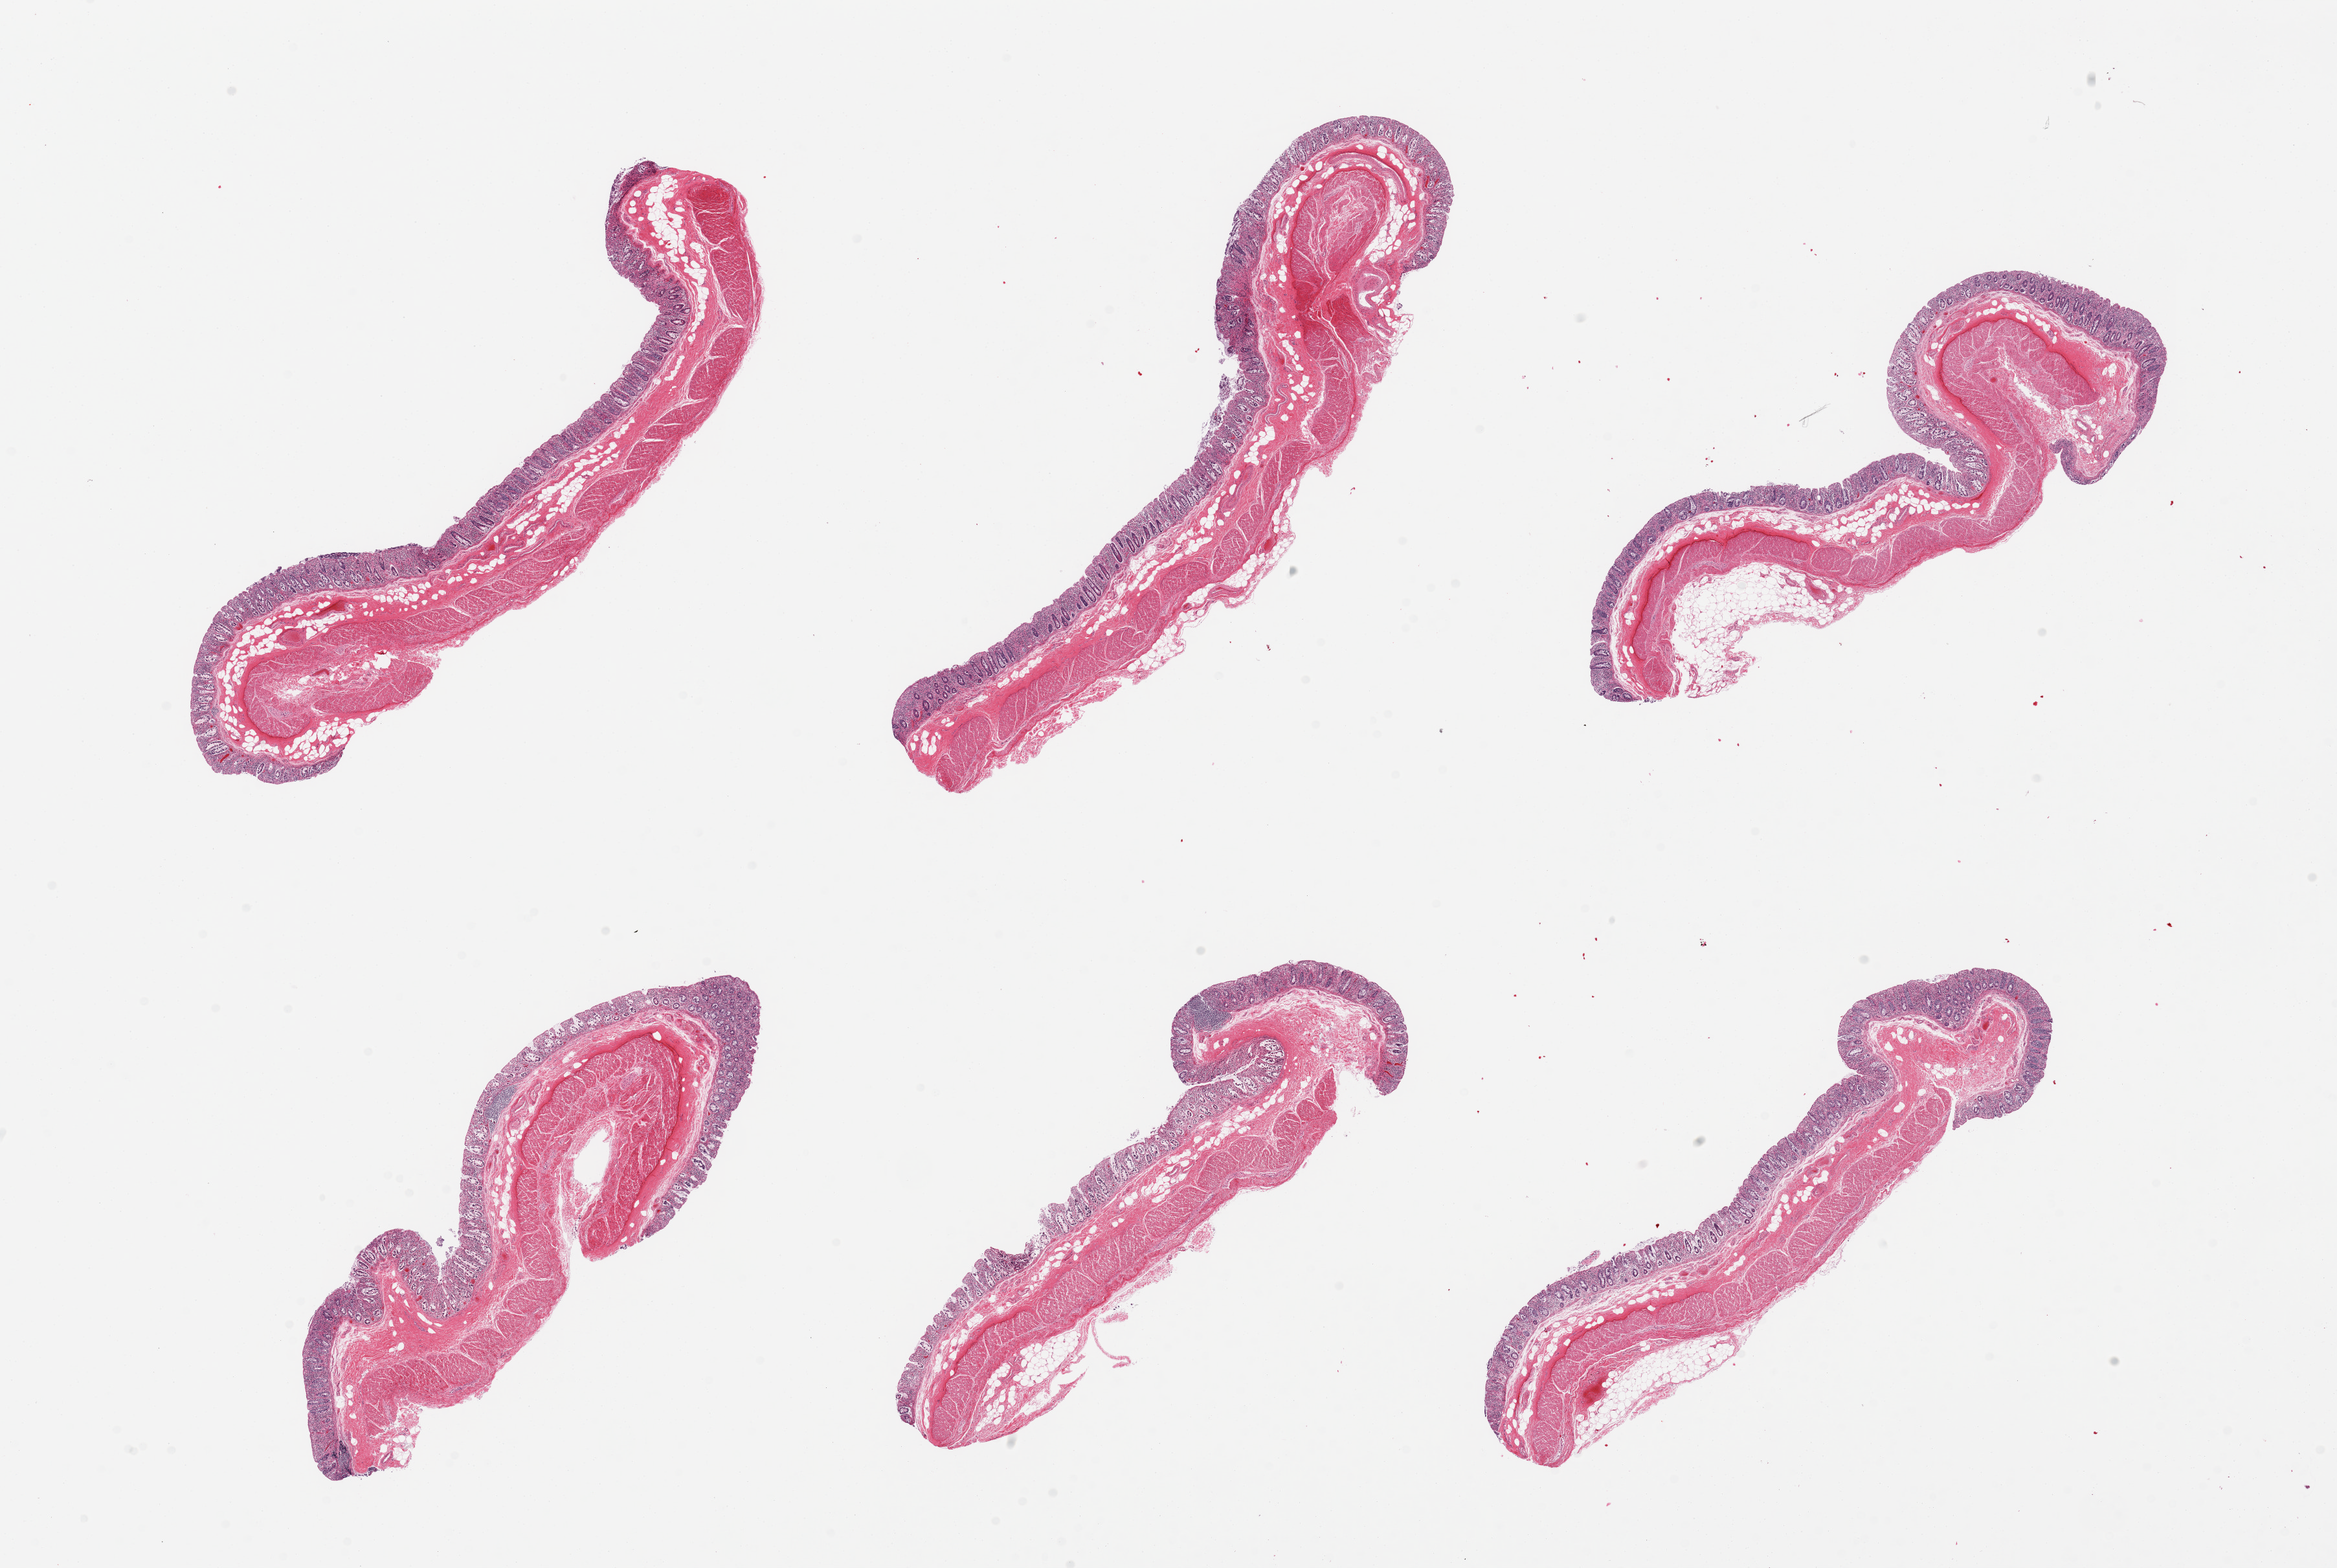
Hematoxylin and eosin (H&E) whole-slide image, shown as a low-resolution overview of the whole scanned area (about 28.5 x 19.2 mm). PAXgene-fixed paraffin-embedded (PFPE) section. Section of transverse colon (target tissue). Tissue donor sample. Male donor.
Reviewer comment on this tissue sample: 6 pieces, mucosa ~0.5mm thick, ~20% thickness, moderately autolyzed.